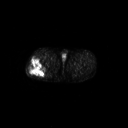
FDG PET of an extremity soft-tissue mass (from a PET/CT study), one axial slice. Slice 256 of 267 in the series (ordered by position). 3.27 mm slice thickness. 128 × 128 image matrix. Patient: male, 43 years. Case-level facts recorded for this patient, not image findings: histological type: poorly differentiated synovial sarcoma; grade: high; site of the primary tumour: right buttock.
Outlined on this slice (expert contour drawn on MRI and transferred to this co-registered scan by the dataset authors):
- gross tumour volume including surrounding oedema: bounding box [x1, y1, x2, y2] px = [28, 57, 47, 77]
- gross tumour volume (mass): [28, 57, 47, 77]